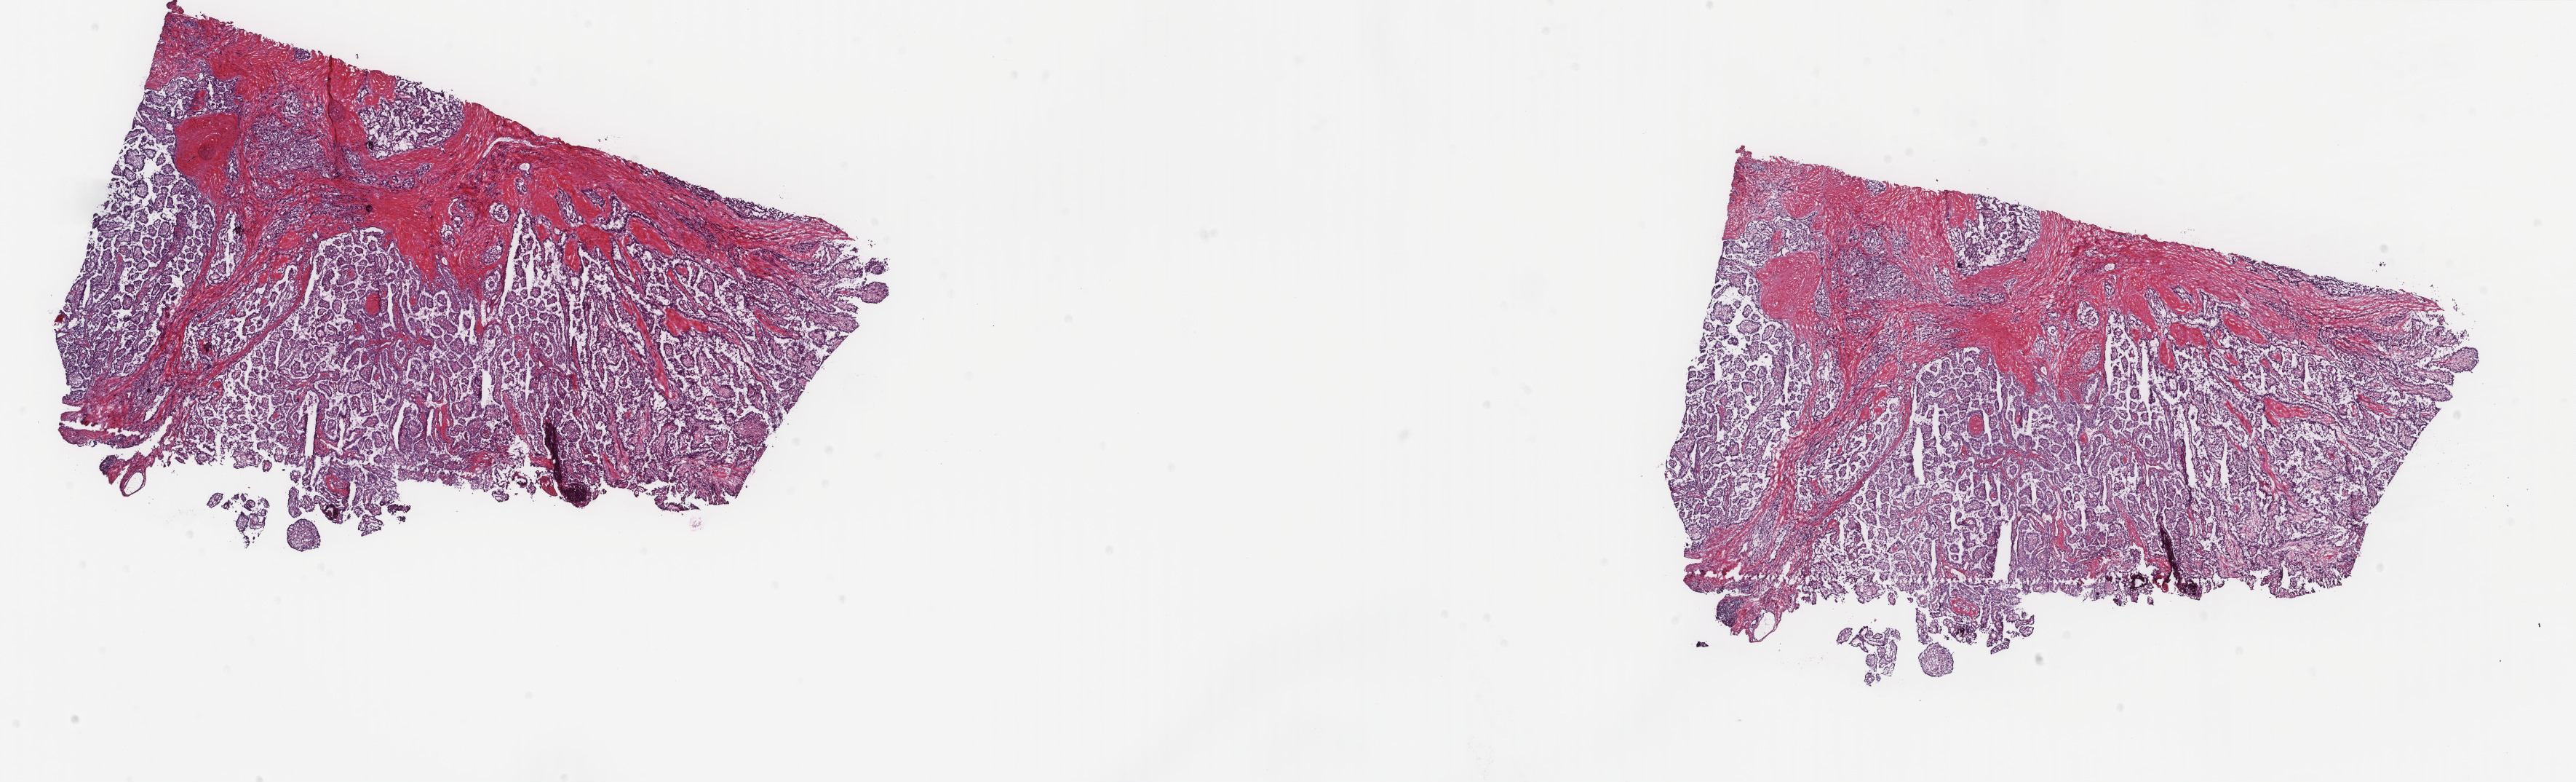
Whole-slide histology image, Hematoxylin and eosin (H&E) stained, low-resolution overview of the scanned area, about 28.1 x 8.5 mm (from a 40x scan), frozen section from the top of the tissue portion, thyroid, primary tumour sample. Patient: male, age at initial diagnosis 22 years. Slide review estimates, as recorded: tumour cells 75%, tumour nuclei 75%, normal cells 0%, stromal cells 25%, necrosis 0%. Inflammatory infiltration, as recorded: lymphocyte infiltration 5%, monocyte infiltration 0%, neutrophil infiltration 0%.
• diagnosis: Nonencapsulated sclerosing carcinoma (thyroid gland)
• TNM: T3 N1a M0
• AJCC pathologic stage: I (7th edition)
• laterality: bilateral